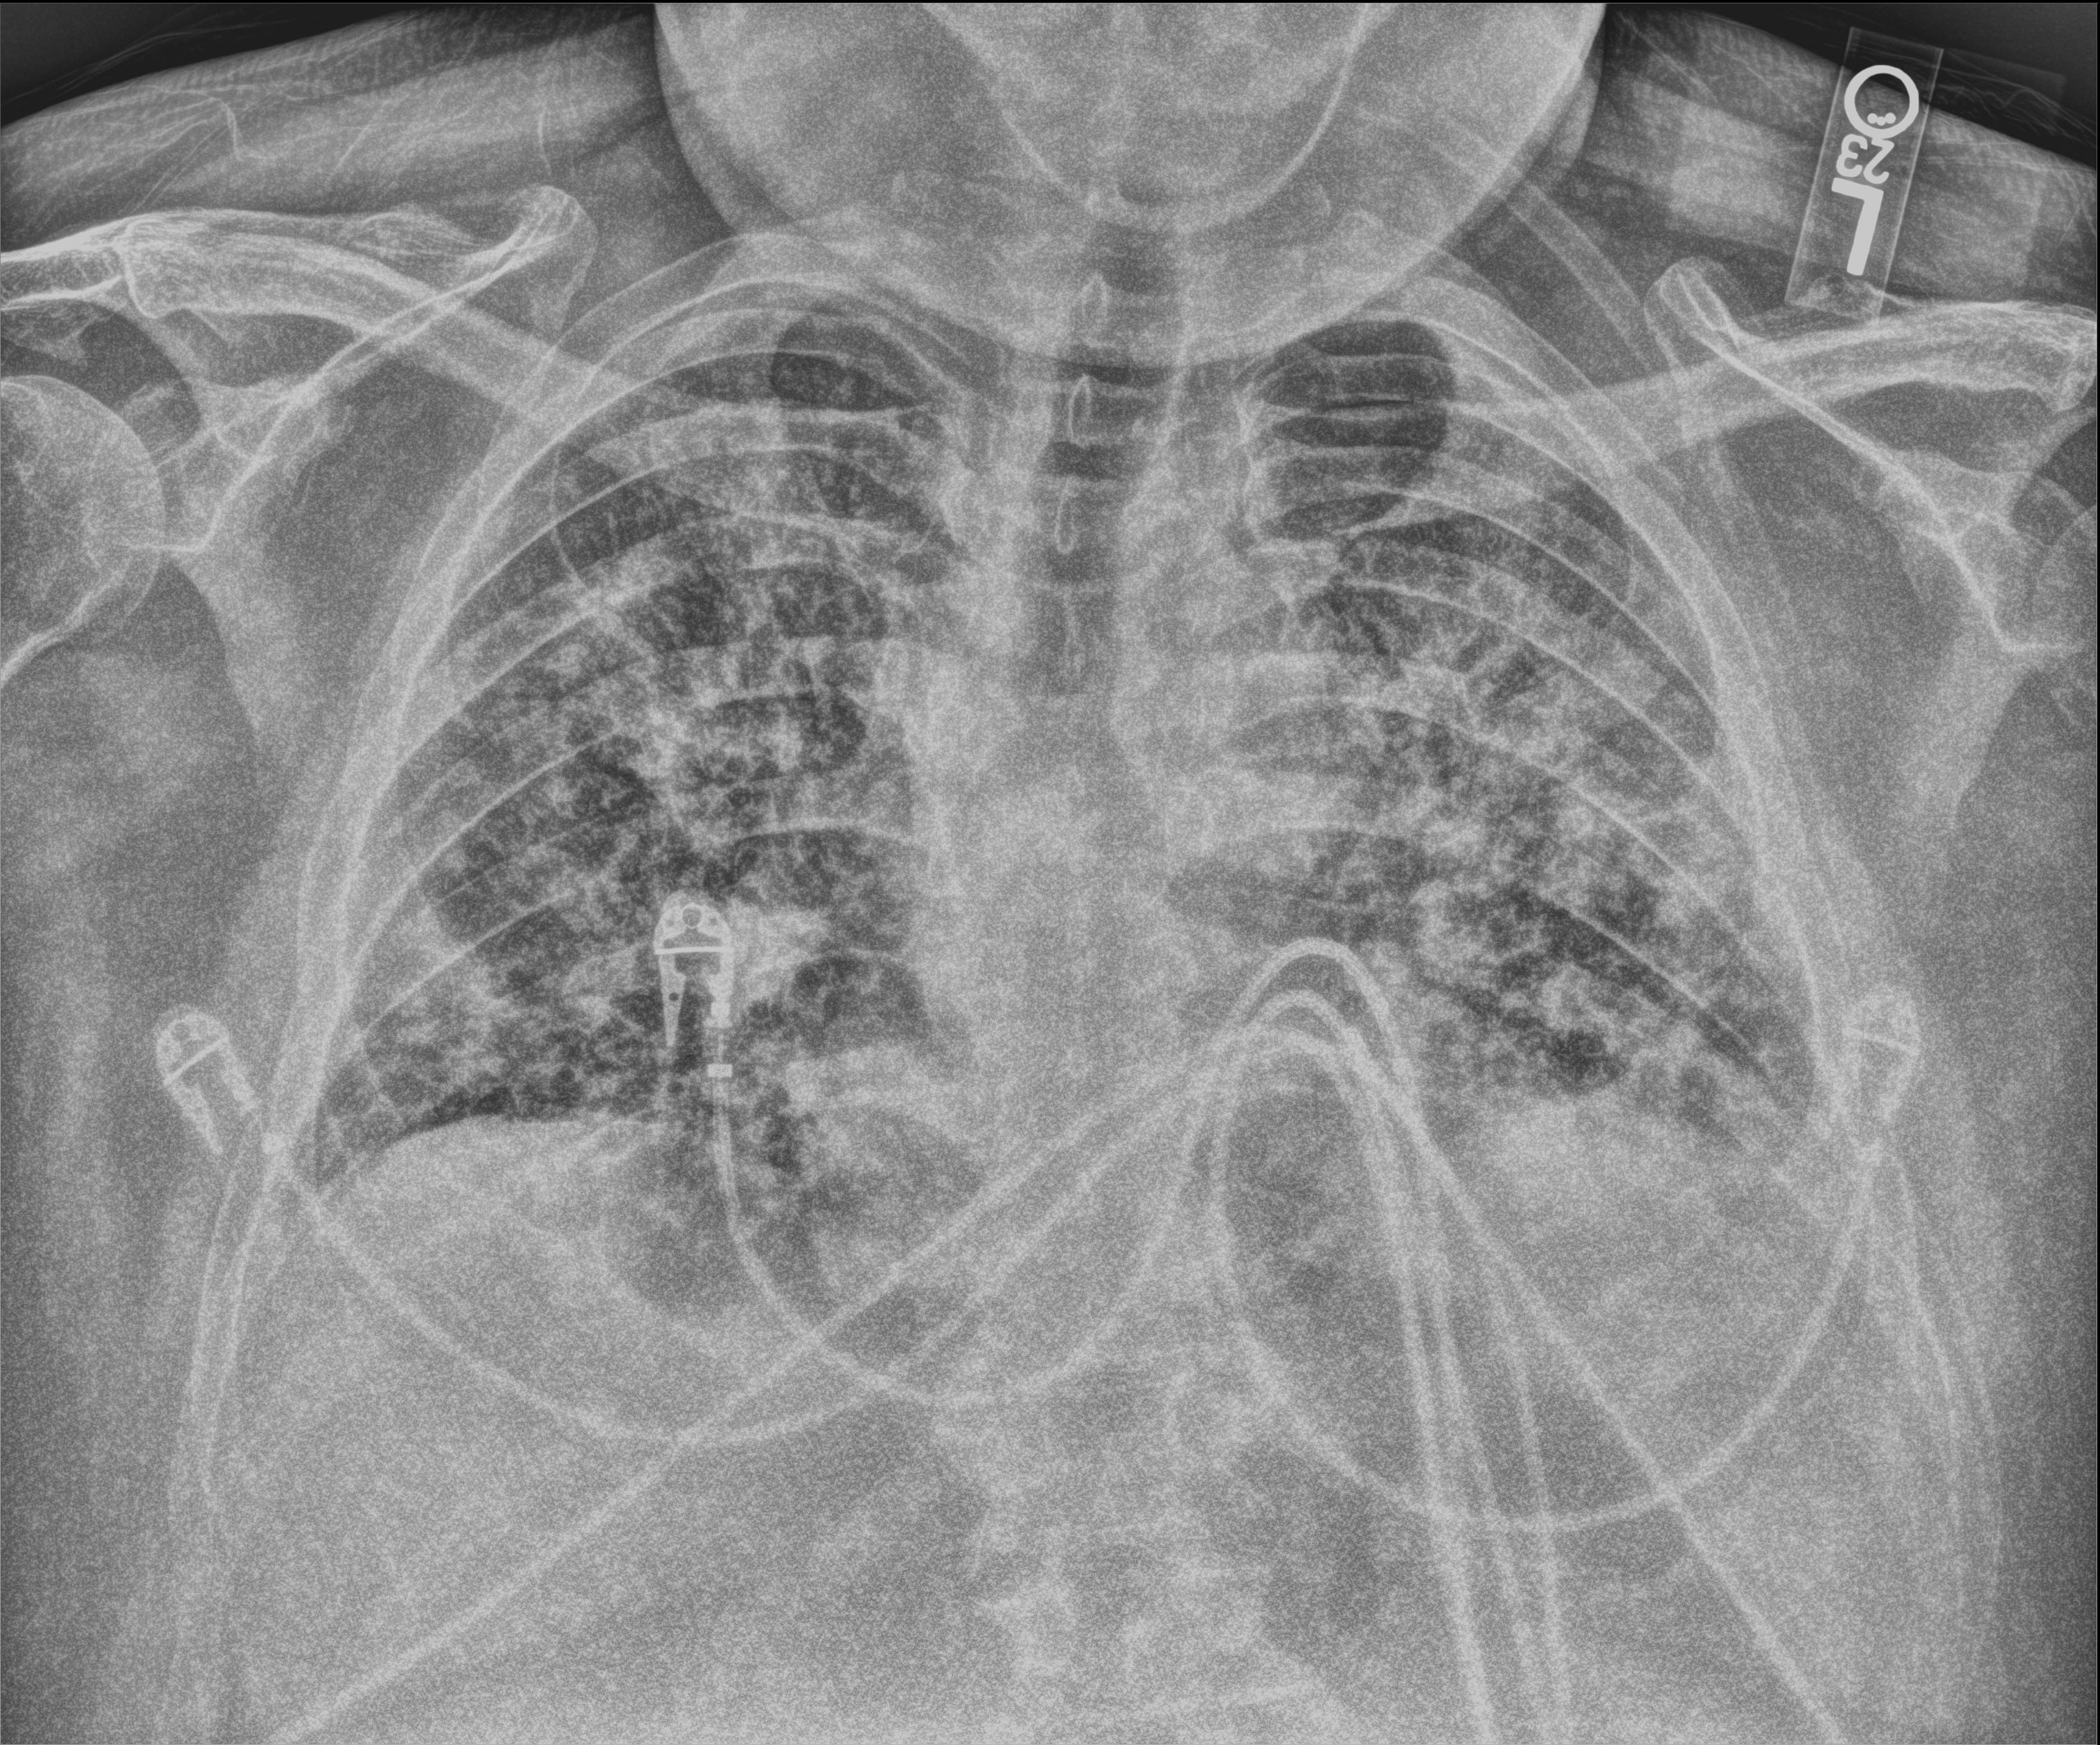
Bedside chest radiograph (computed radiography), anteroposterior (AP) projection. Patient hospitalised with COVID-19; male, aged 18–59 years.
Admission-level facts for this patient (not findings on this image; timing relative to this image not recorded): admitted to intensive care during this hospital stay: no; mechanically ventilated during this hospital stay: no; other chronic lung disease (admission record): no.